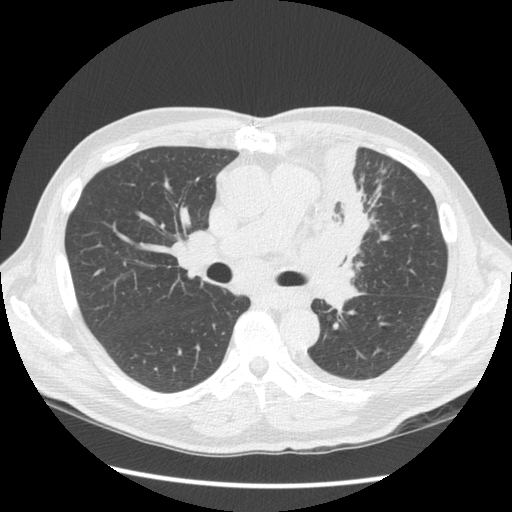
Low-dose screening chest CT, one axial slice. 120 kVp. Lung window (W 1500 / L -600 HU). 2.5 mm slice thickness. 512 × 512 image matrix, field of view 360 × 360 mm.
Outlined on this slice (outlined manually by an expert reader):
- lesion 1 (tumor, upper lobe of left lung): bounding box <297,140,371,312> (left, top, right, bottom; pixels)